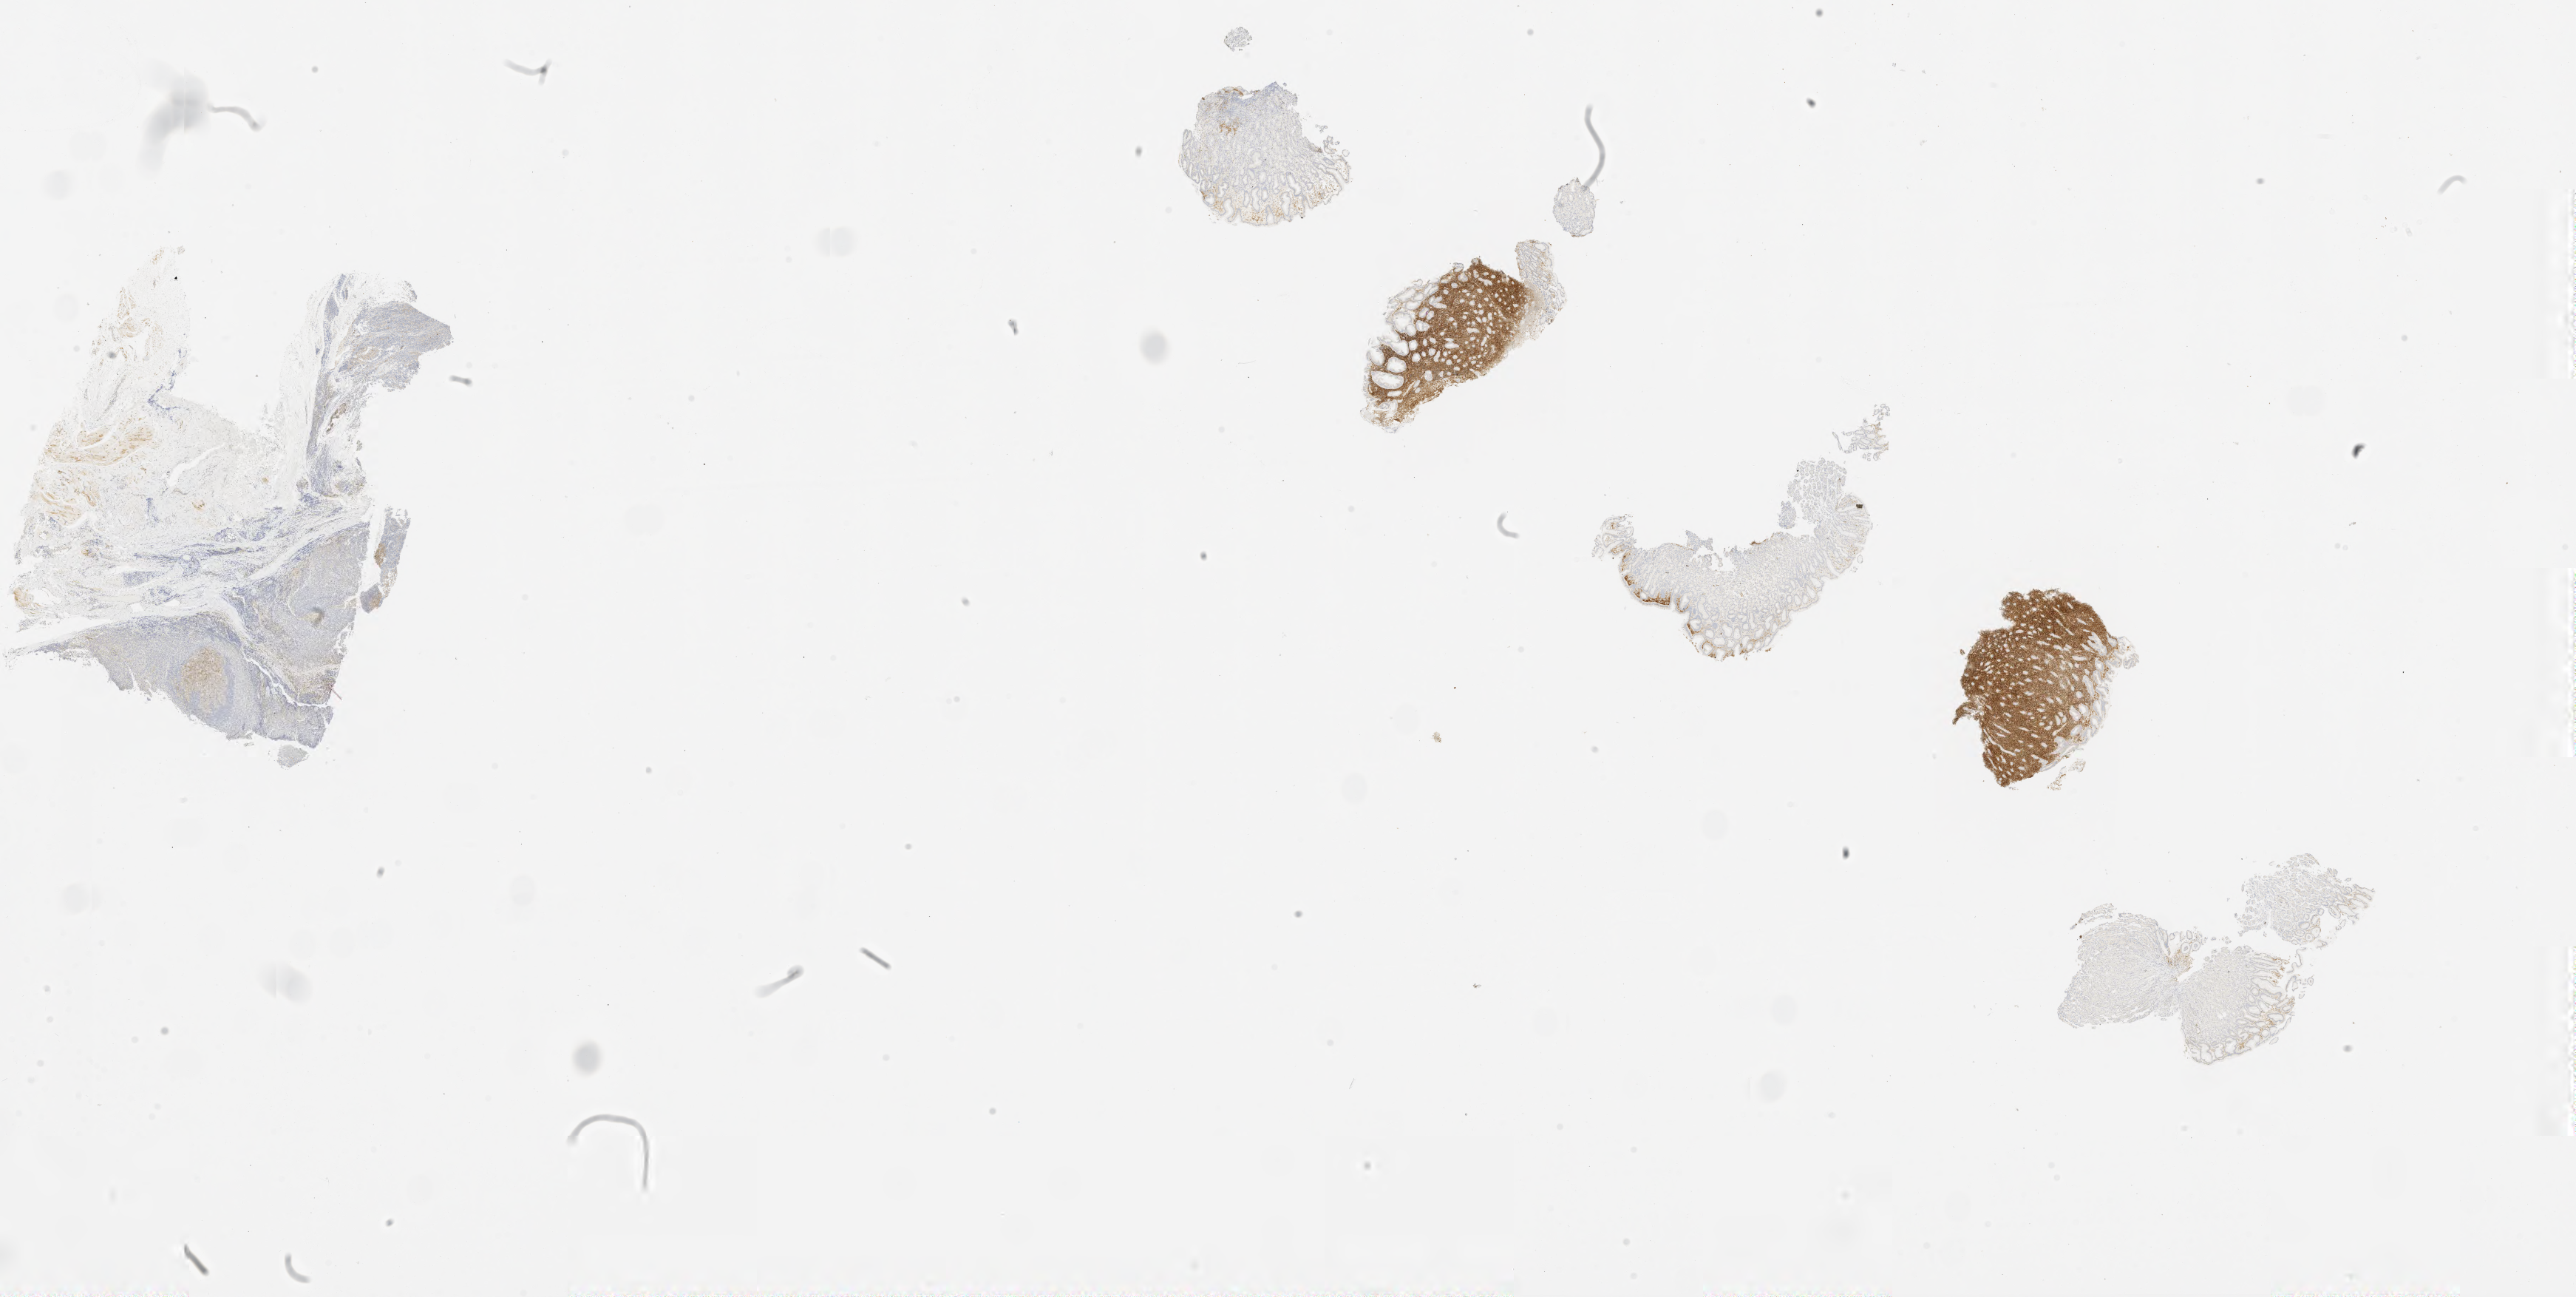
Immunohistochemistry (IHC) whole-slide image stained for CD10, whole scanned area (about 28.0 x 14.1 mm) shown as a low-resolution overview; specimen: tumor tissue. Patient male; aged 40.
* diagnosis: Burkitt lymphoma, NOS